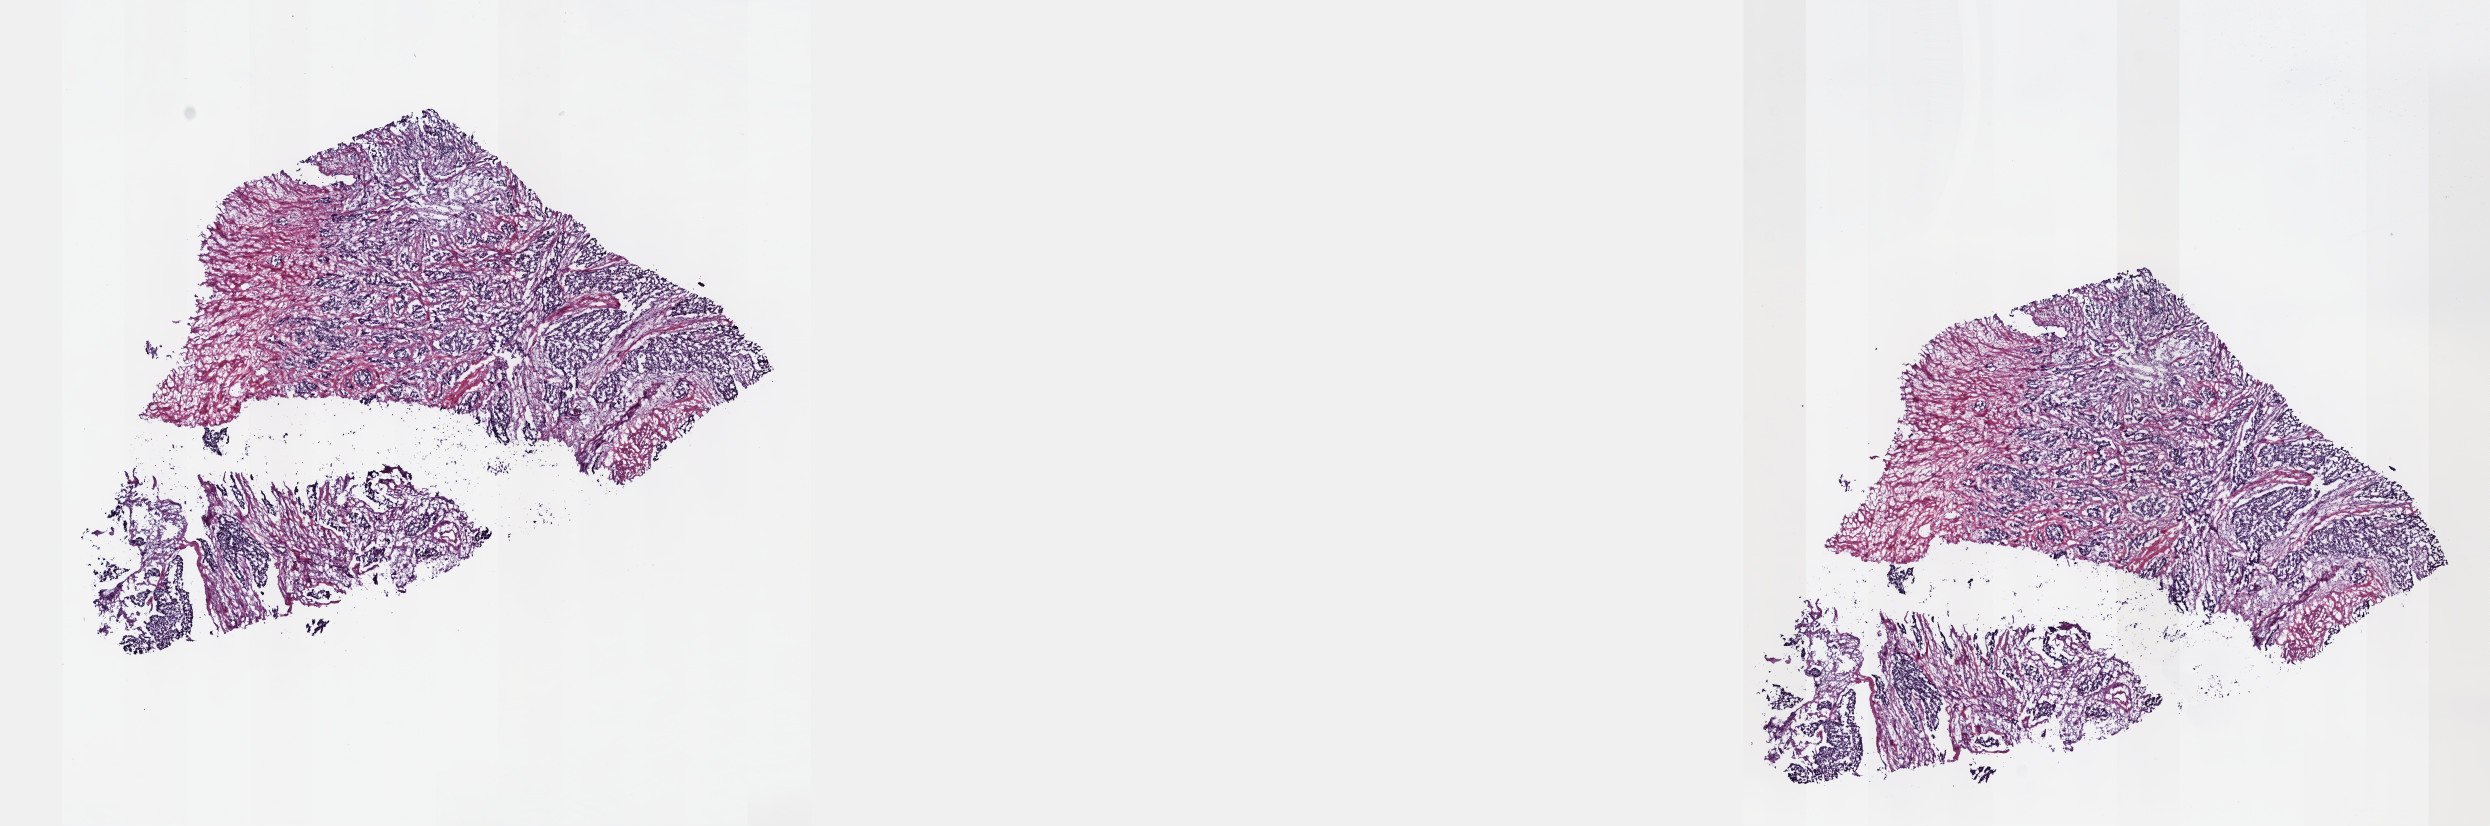
Digitized H&E tissue section (whole slide), low-resolution overview of the scanned area, about 20.1 x 6.7 mm (from a 40x scan), frozen section from the top of the tissue portion, bladder, primary tumour sample. Male patient; age at initial diagnosis 67 years. Histologic grade: high grade. Pathologist review of this section (percent, as recorded): tumour cells 75%, tumour nuclei 75%, normal cells 0%, stromal cells 25%, necrosis 0%. Inflammatory infiltration, as recorded: lymphocyte infiltration 2%, monocyte infiltration 1%, neutrophil infiltration 3%.
* pathologic diagnosis: Transitional cell carcinoma
* AJCC pathologic stage: IV (6th edition)